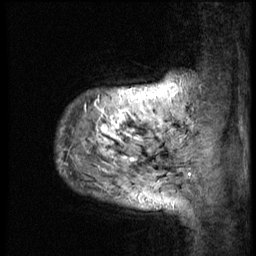
Breast MRI (dynamic contrast-enhanced), one sagittal slice. Position 6 of 58 along the scan axis. 3 images stored at this slice position (order not interpretable as contrast timing). 1.5 T. TE 4.2 ms, TR 9 ms. 2.5 mm slice thickness. 256 × 256 image matrix, field of view 180 × 180 mm. Patient: female, 50 years. From the clinical record (not read from this slice): setting: breast cancer imaged before/during neoadjuvant chemotherapy; receptor status: triple-negative.
Structures marked on this image (semi-automatically segmented with operator editing):
- analysis volume of interest (the breast-tissue region the enhancement analysis was run in; not a lesion): bounding box <56,62,186,214> (left, top, right, bottom; pixels)
- tumour enhancement mask (voxels above the 140 % enhancement threshold inside the analysis volume of interest): <89,88,167,159>